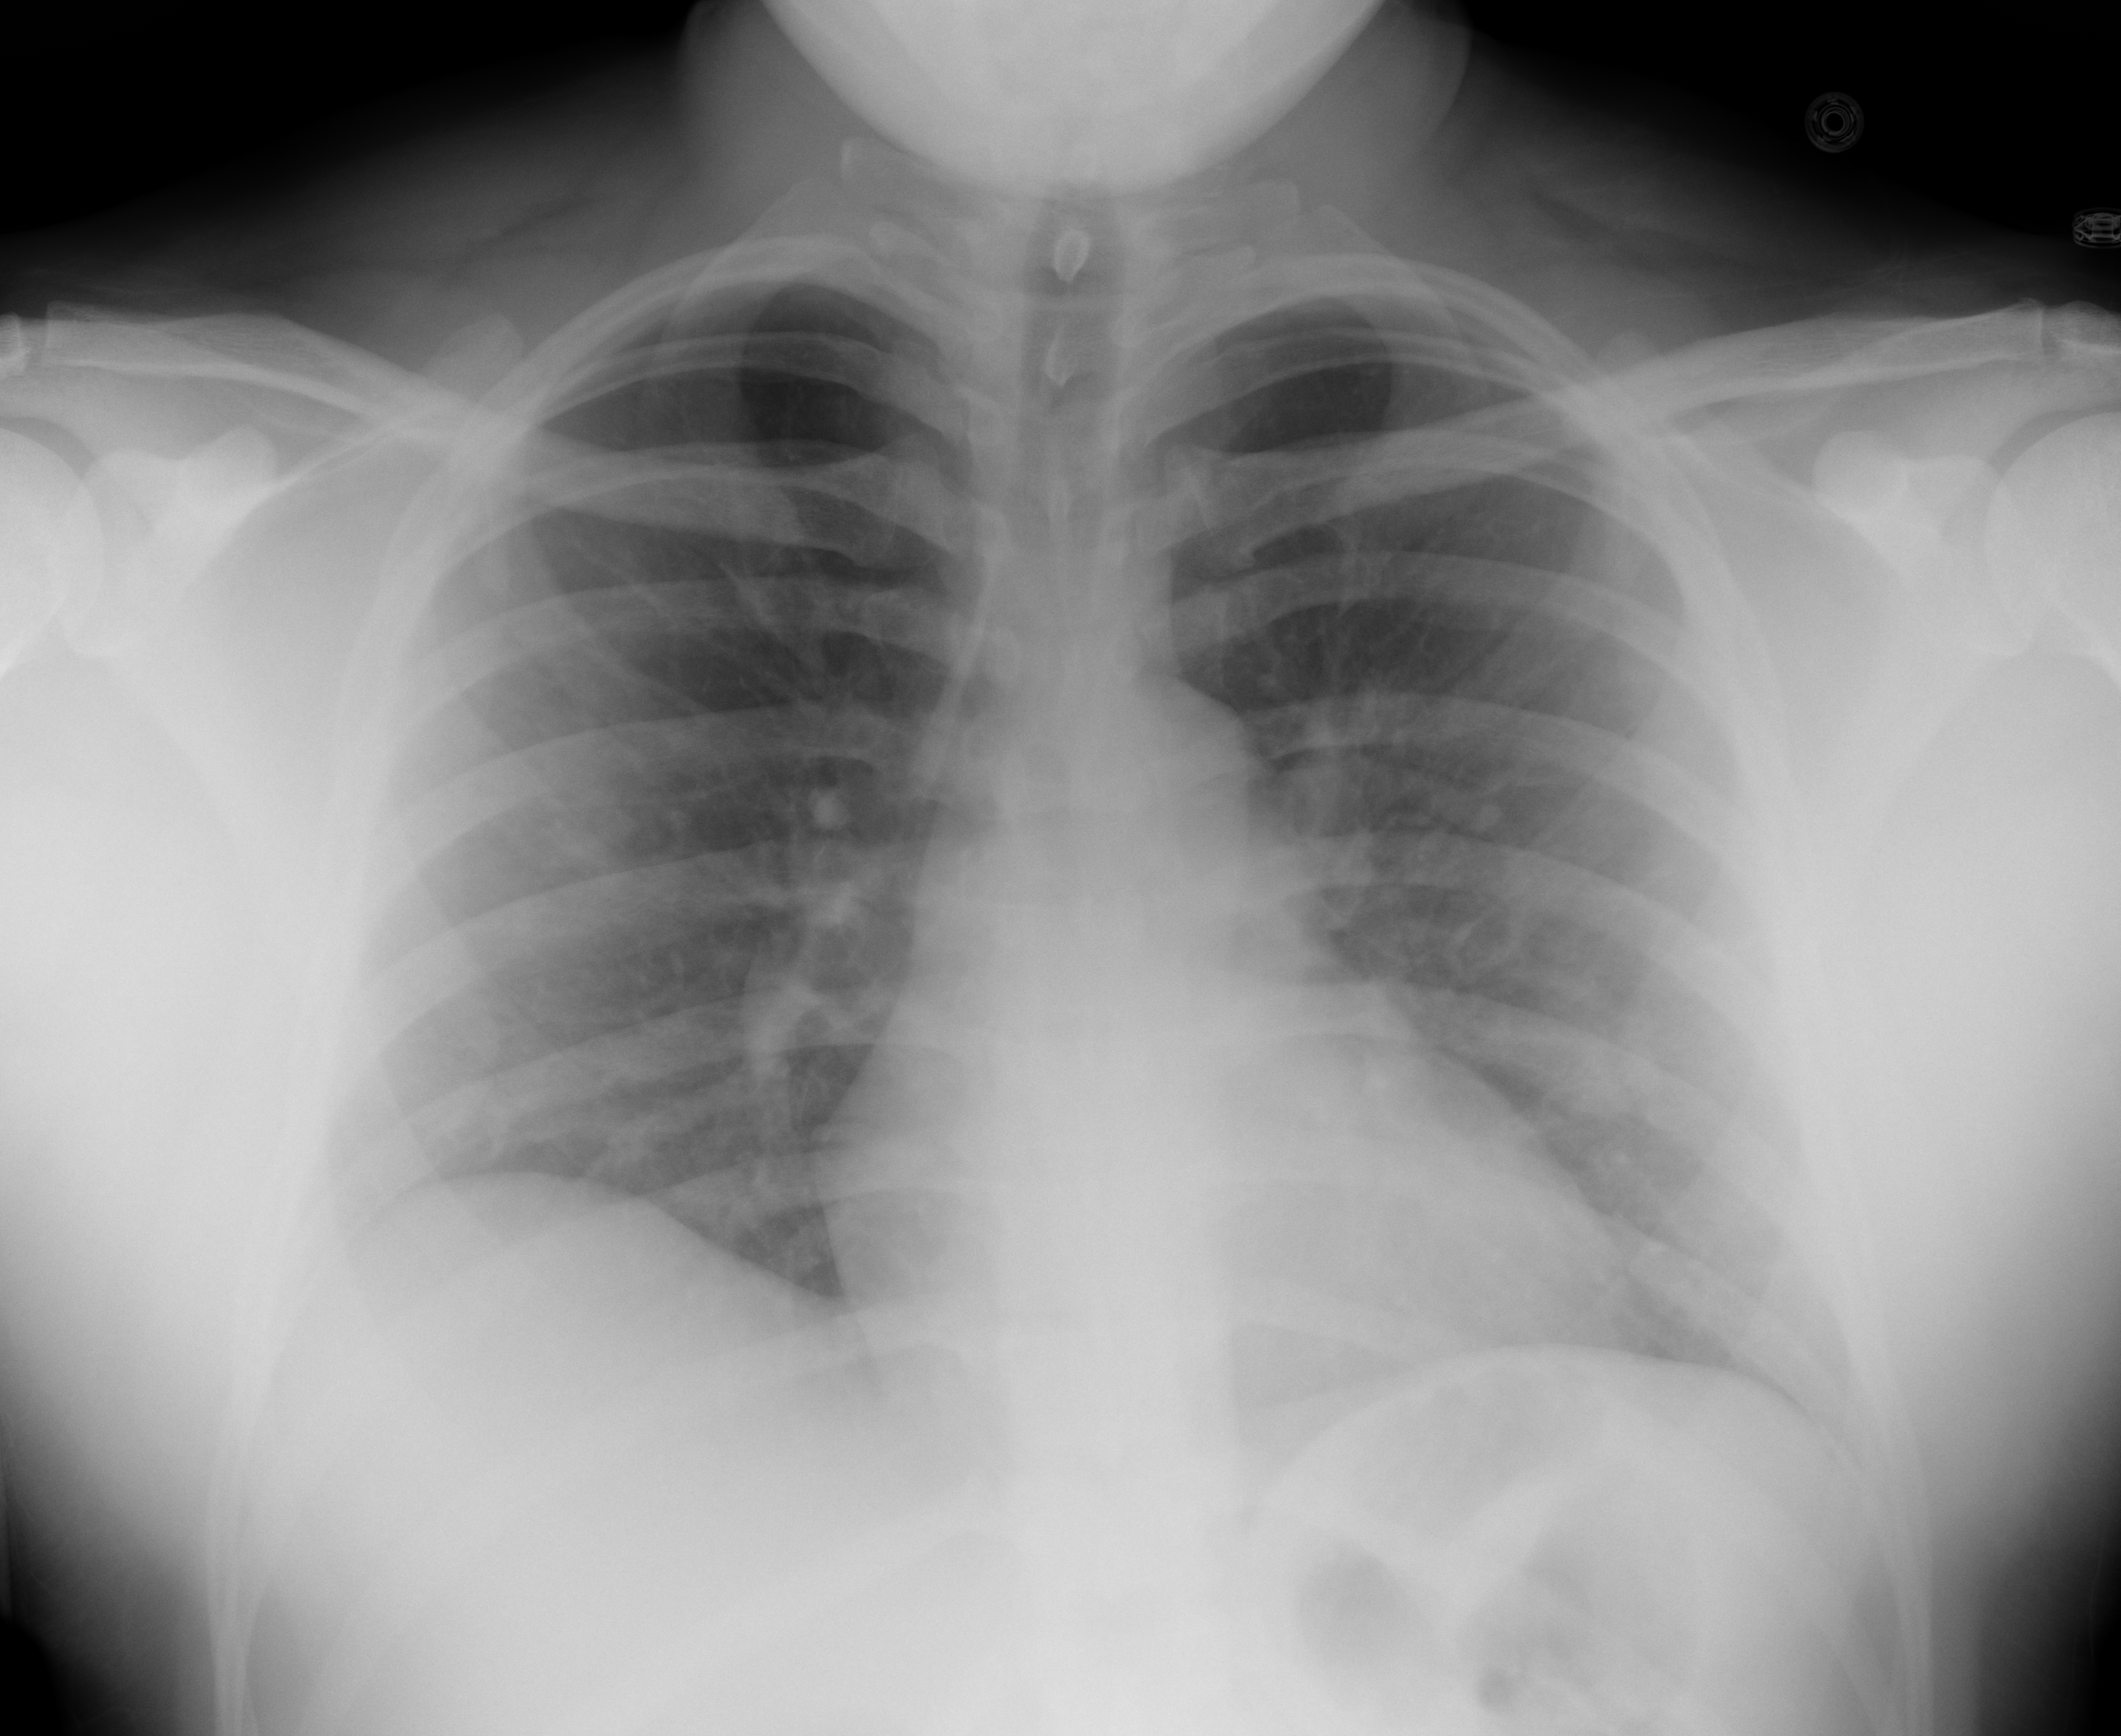
Portable chest radiograph, AP projection. Male patient, age 37 years; imaged 15 days after the COVID-19 diagnosis.
Radiologist's key findings for this exam: no acute disease, no focal pneumonia.